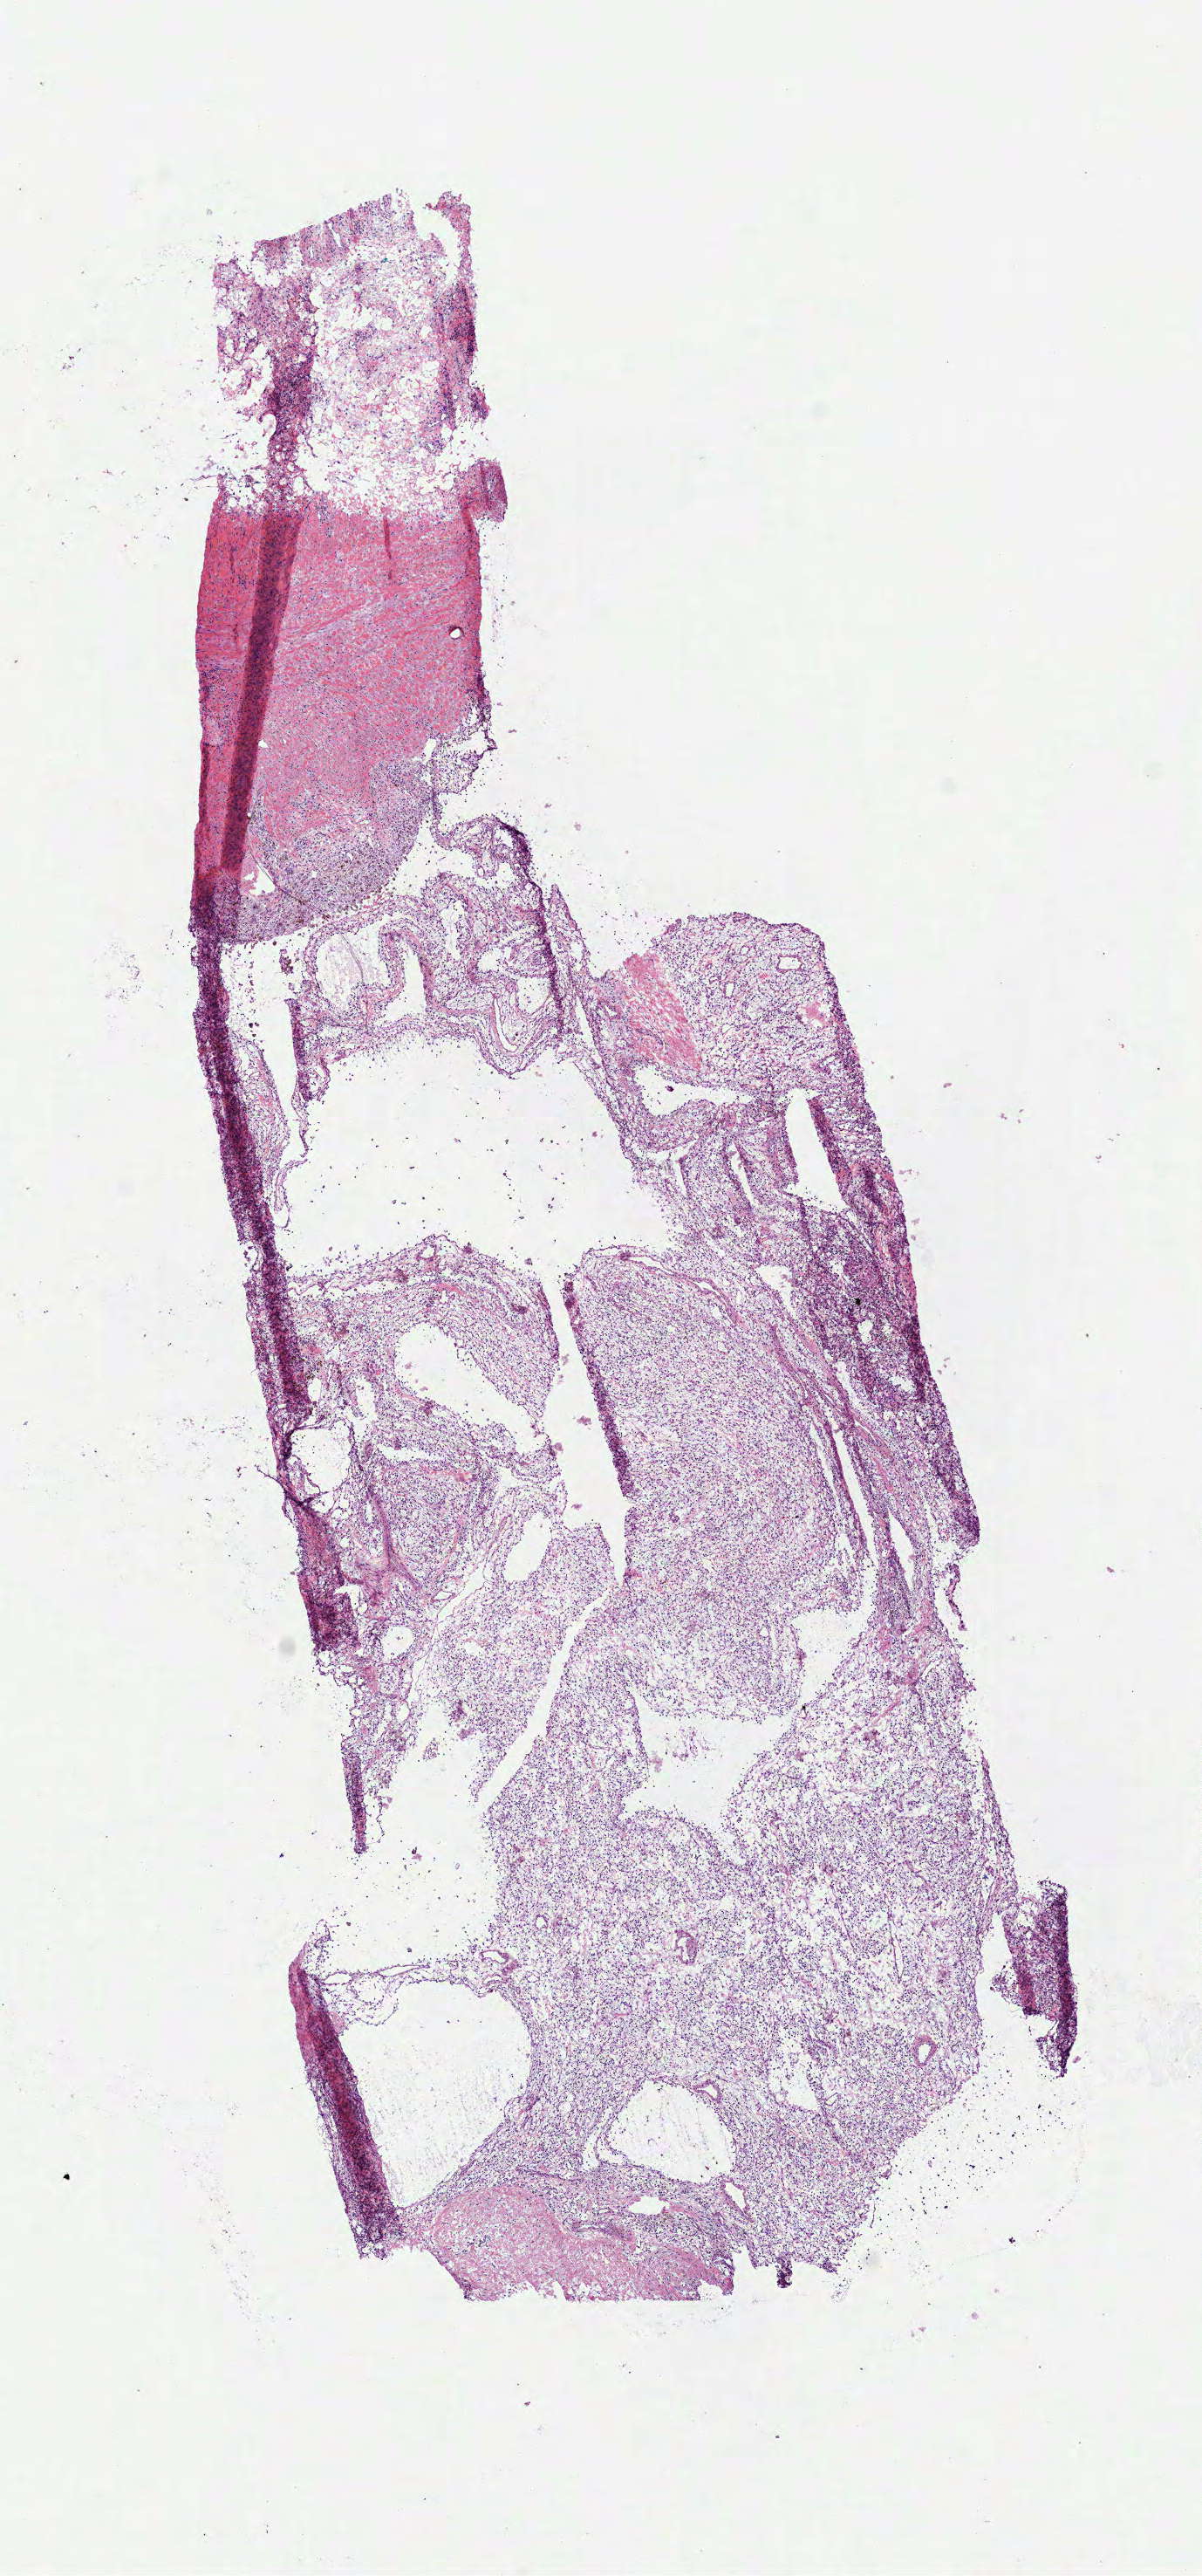
Hematoxylin and eosin (H&E) stained whole-slide image — a low-resolution overview of the entire scanned area, about 5.6 x 11.9 mm. Frozen section. Primary tumour sample from the kidney. Patient: female, age at initial diagnosis 41 years. Histologic grade: G2 (moderately differentiated). Slide review estimates, as recorded: tumour cells 85%, tumour nuclei 85%, normal cells 0%, stromal cells 15%, necrosis 0%.
AJCC pathologic stage: I. TNM: T1b NX M0. Diagnosis: Clear cell adenocarcinoma, NOS.